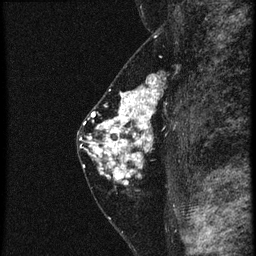
Breast MRI (dynamic contrast-enhanced), one sagittal slice; slice 33 of 60 in the series (ordered by position); 4 images stored at this slice position (order not interpretable as contrast timing); 1.5 T; TE 4.2 ms, TR 20.4 ms; 256 × 256 image matrix, field of view 180 × 180 mm. Female patient, age 46 years. Case-level facts recorded for this patient, not image findings: setting: breast cancer imaged before/during neoadjuvant chemotherapy; receptor status: triple-negative.
Outlined on this slice (semi-automatically segmented with operator editing):
- analysis volume of interest (the breast-tissue region the enhancement analysis was run in; not a lesion): box from (x=88, y=82) to (x=175, y=185) px
- tumour enhancement mask (voxels above the 90 % enhancement threshold inside the analysis volume of interest): (x=88, y=82)–(x=161, y=183)